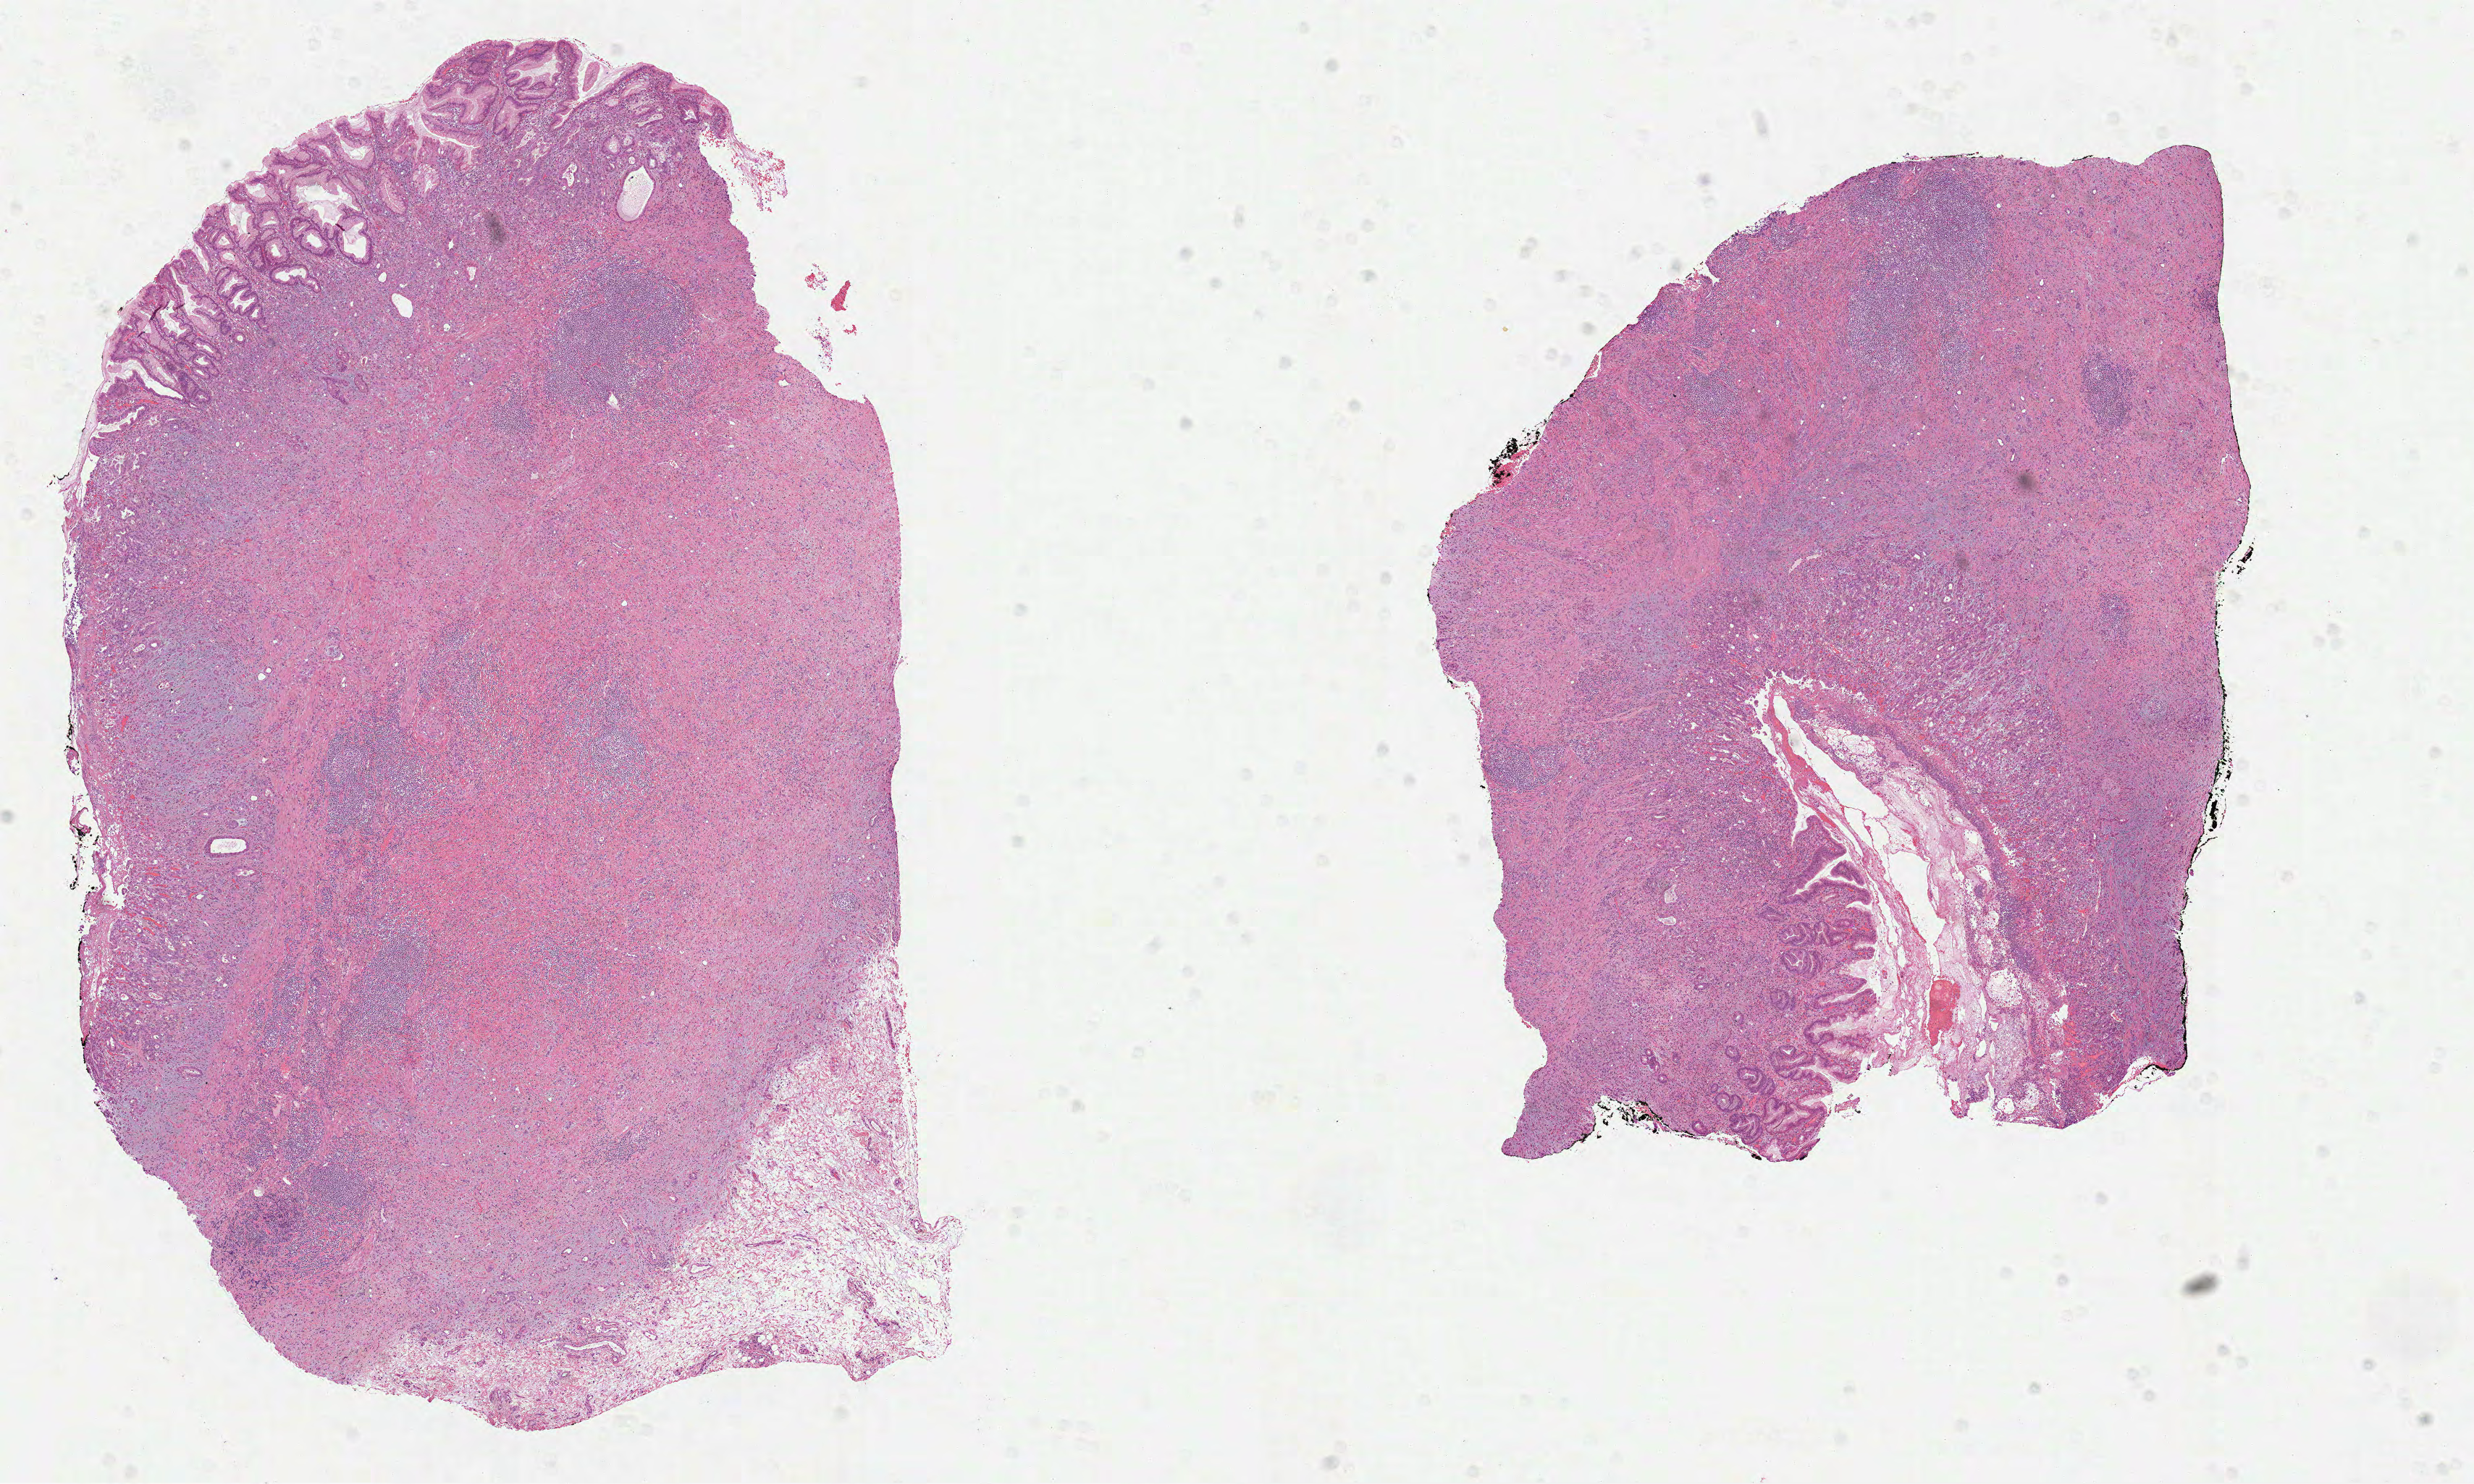
Whole-slide histology image, H&E — a low-resolution overview of the entire scanned area, about 13.8 x 8.3 mm; formalin-fixed paraffin-embedded (FFPE) diagnostic section; stomach, primary tumour sample. Patient: male, age at initial diagnosis 49 years. Histologic grade: G3 (poorly differentiated).
Lymph nodes positive (case pathology): 0 of 5 examined. AJCC pathologic stage: IB (6th edition). Pathologic diagnosis: Carcinoma, diffuse type (gastric antrum).